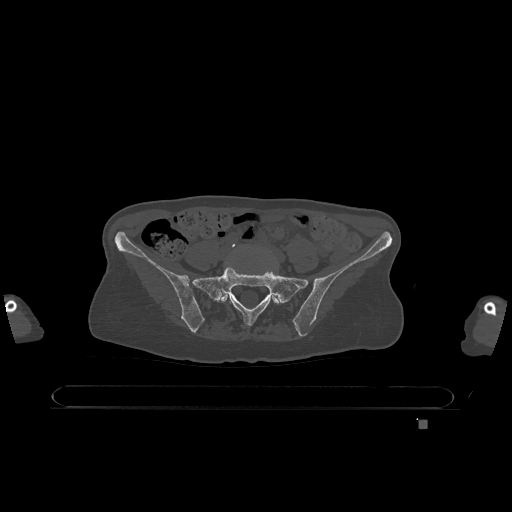
CT including the spine, one axial slice. Slice 203 of 1317 in the series (ordered by position). Bone window (W 1800 / L 400 HU). 0.5 mm slice thickness. 512 × 512 image matrix, field of view 500 × 500 mm. Female patient, age 74 years. From the clinical record (not read from this slice): primary cancer: lung; vertebrae with lytic lesions (as recorded): T1, T4, T5, T6, L4, L5.
Structures marked on this image (semi-automatically segmented with operator editing):
- L5 vertebra: bounding box [x1, y1, x2, y2] px = [219, 247, 280, 304]